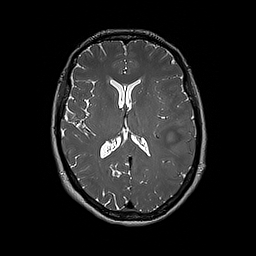
Brain MRI from a brain-tumour surgery series, one axial slice; position 95 of 192 along the scan axis; 1 mm slice thickness; 256 × 256 image matrix, field of view 250 × 250 mm. Case-level facts recorded for this patient, not image findings: histopathology: Glioblastoma; WHO grade: 4; IDH mutation: no; tumour location: Left Frontal.
Outlined on this slice (manually delineated by an expert):
- tumour: bounding box [x1, y1, x2, y2] px = [177, 131, 194, 169]